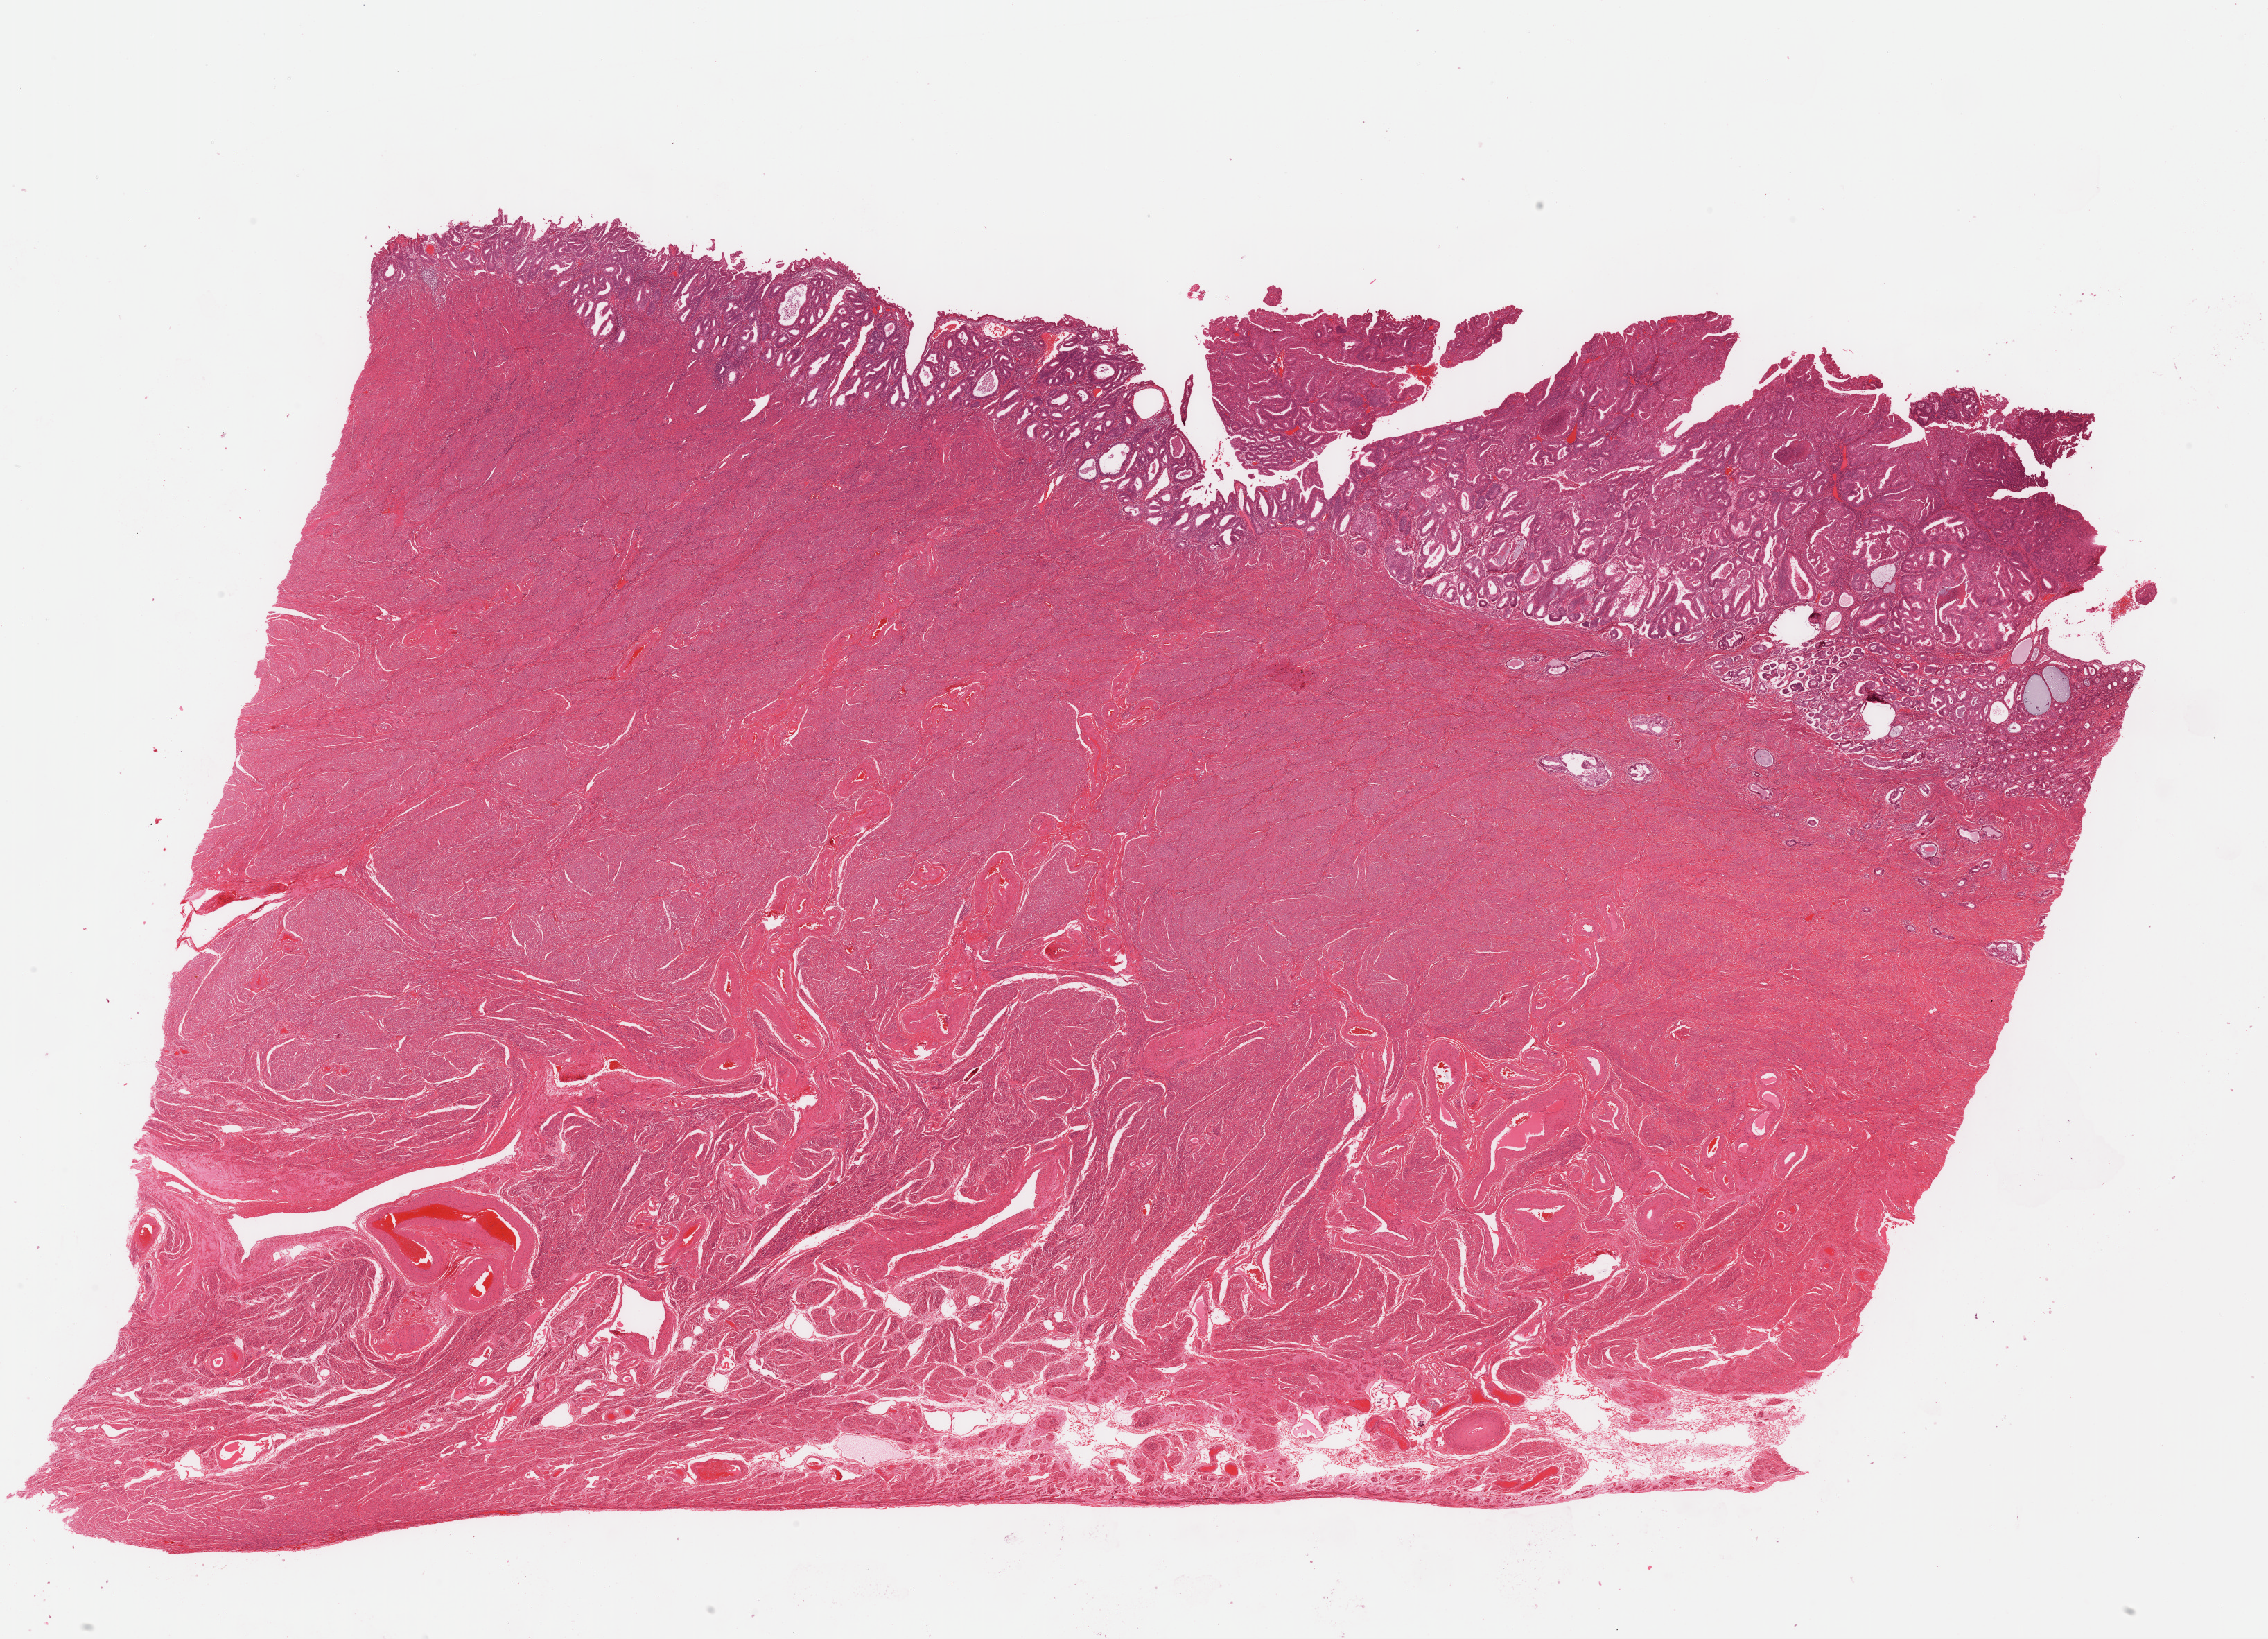
Whole-slide histology image, H&E, low-resolution overview of the scanned area, about 25.8 x 18.7 mm (acquisition: 40x scan). Formalin-fixed paraffin-embedded (FFPE) diagnostic section. Sample: primary tumour, uterus. Female patient; age at initial diagnosis 57 years. Histologic grade: G1 (well differentiated).
FIGO stage: IB. Histologic diagnosis: Endometrioid adenocarcinoma, NOS. Lymph nodes positive (case pathology): 0 of 24 examined.